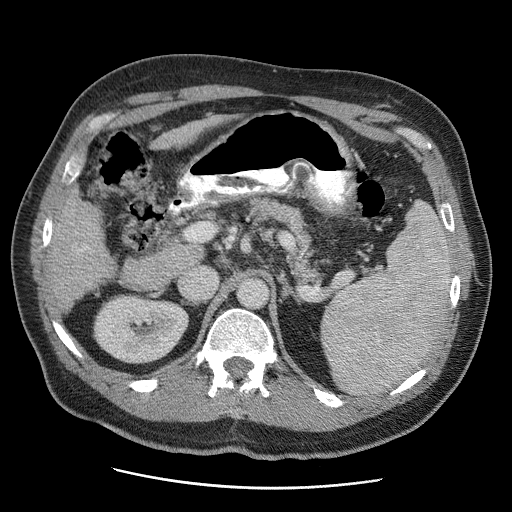
Contrast-enhanced abdominal CT (liver protocol), one axial slice. Position 20 of 81 along the scan axis. Reconstruction kernel STANDARD. 120 kVp. Soft-tissue window (W 400 / L 40 HU). 512 × 512 image matrix, field of view 380 × 380 mm. From the clinical record (not read from this slice): diagnosis: hepatocellular carcinoma (patient treated with transarterial chemoembolisation; whether this scan precedes or follows treatment is not stated here); TNM stage (as recorded): Stage-IIIA; Child-Pugh class: A; tumour nodularity: multinodular; tumour size: 5.5 cm.
Structures marked on this image (semi-automatically segmented with operator editing):
- liver parenchyma outside the tumour (the mass and vessels are separate outlines, so this box may not span the whole liver): bounding box <48,116,223,310> (left, top, right, bottom; pixels)